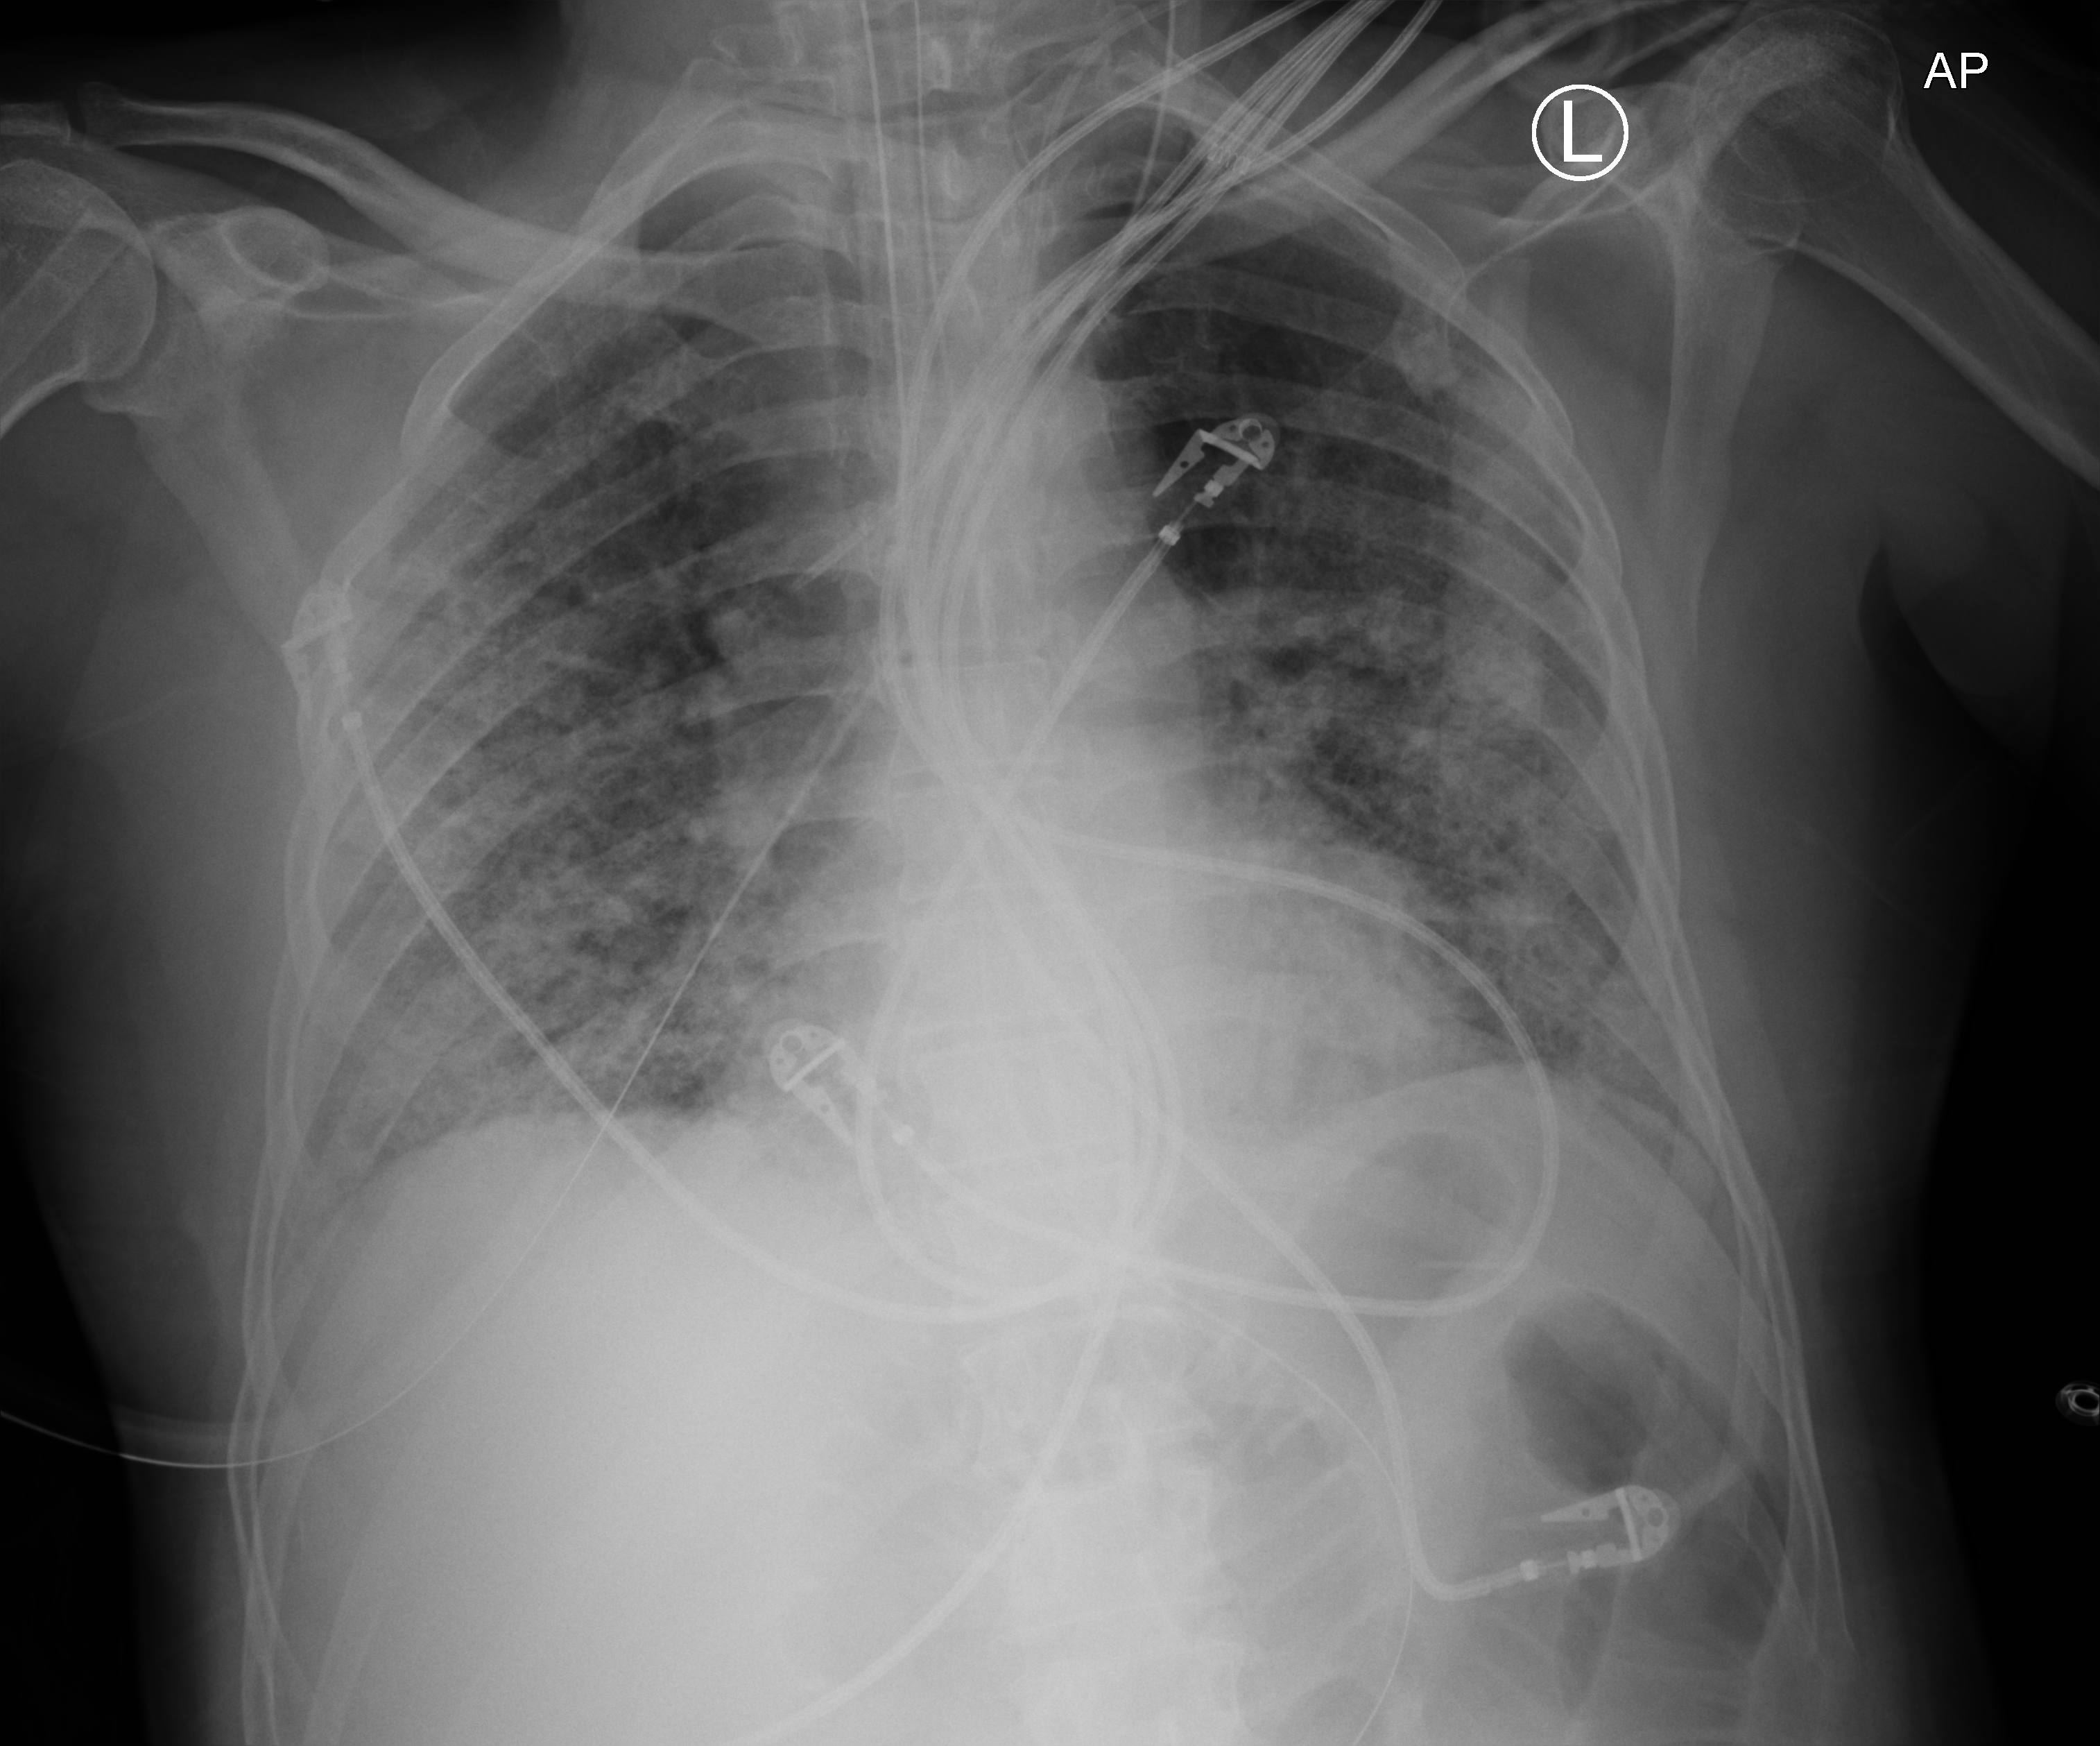
Bedside chest radiograph (computed radiography), anteroposterior (AP) projection. Patient hospitalised with COVID-19; male, aged 60–74 years.
From the hospital-stay record, not from the radiograph (when in the stay this image was taken is not recorded): admitted to intensive care during this hospital stay: yes; mechanically ventilated during this hospital stay: yes; other chronic lung disease (admission record): yes.